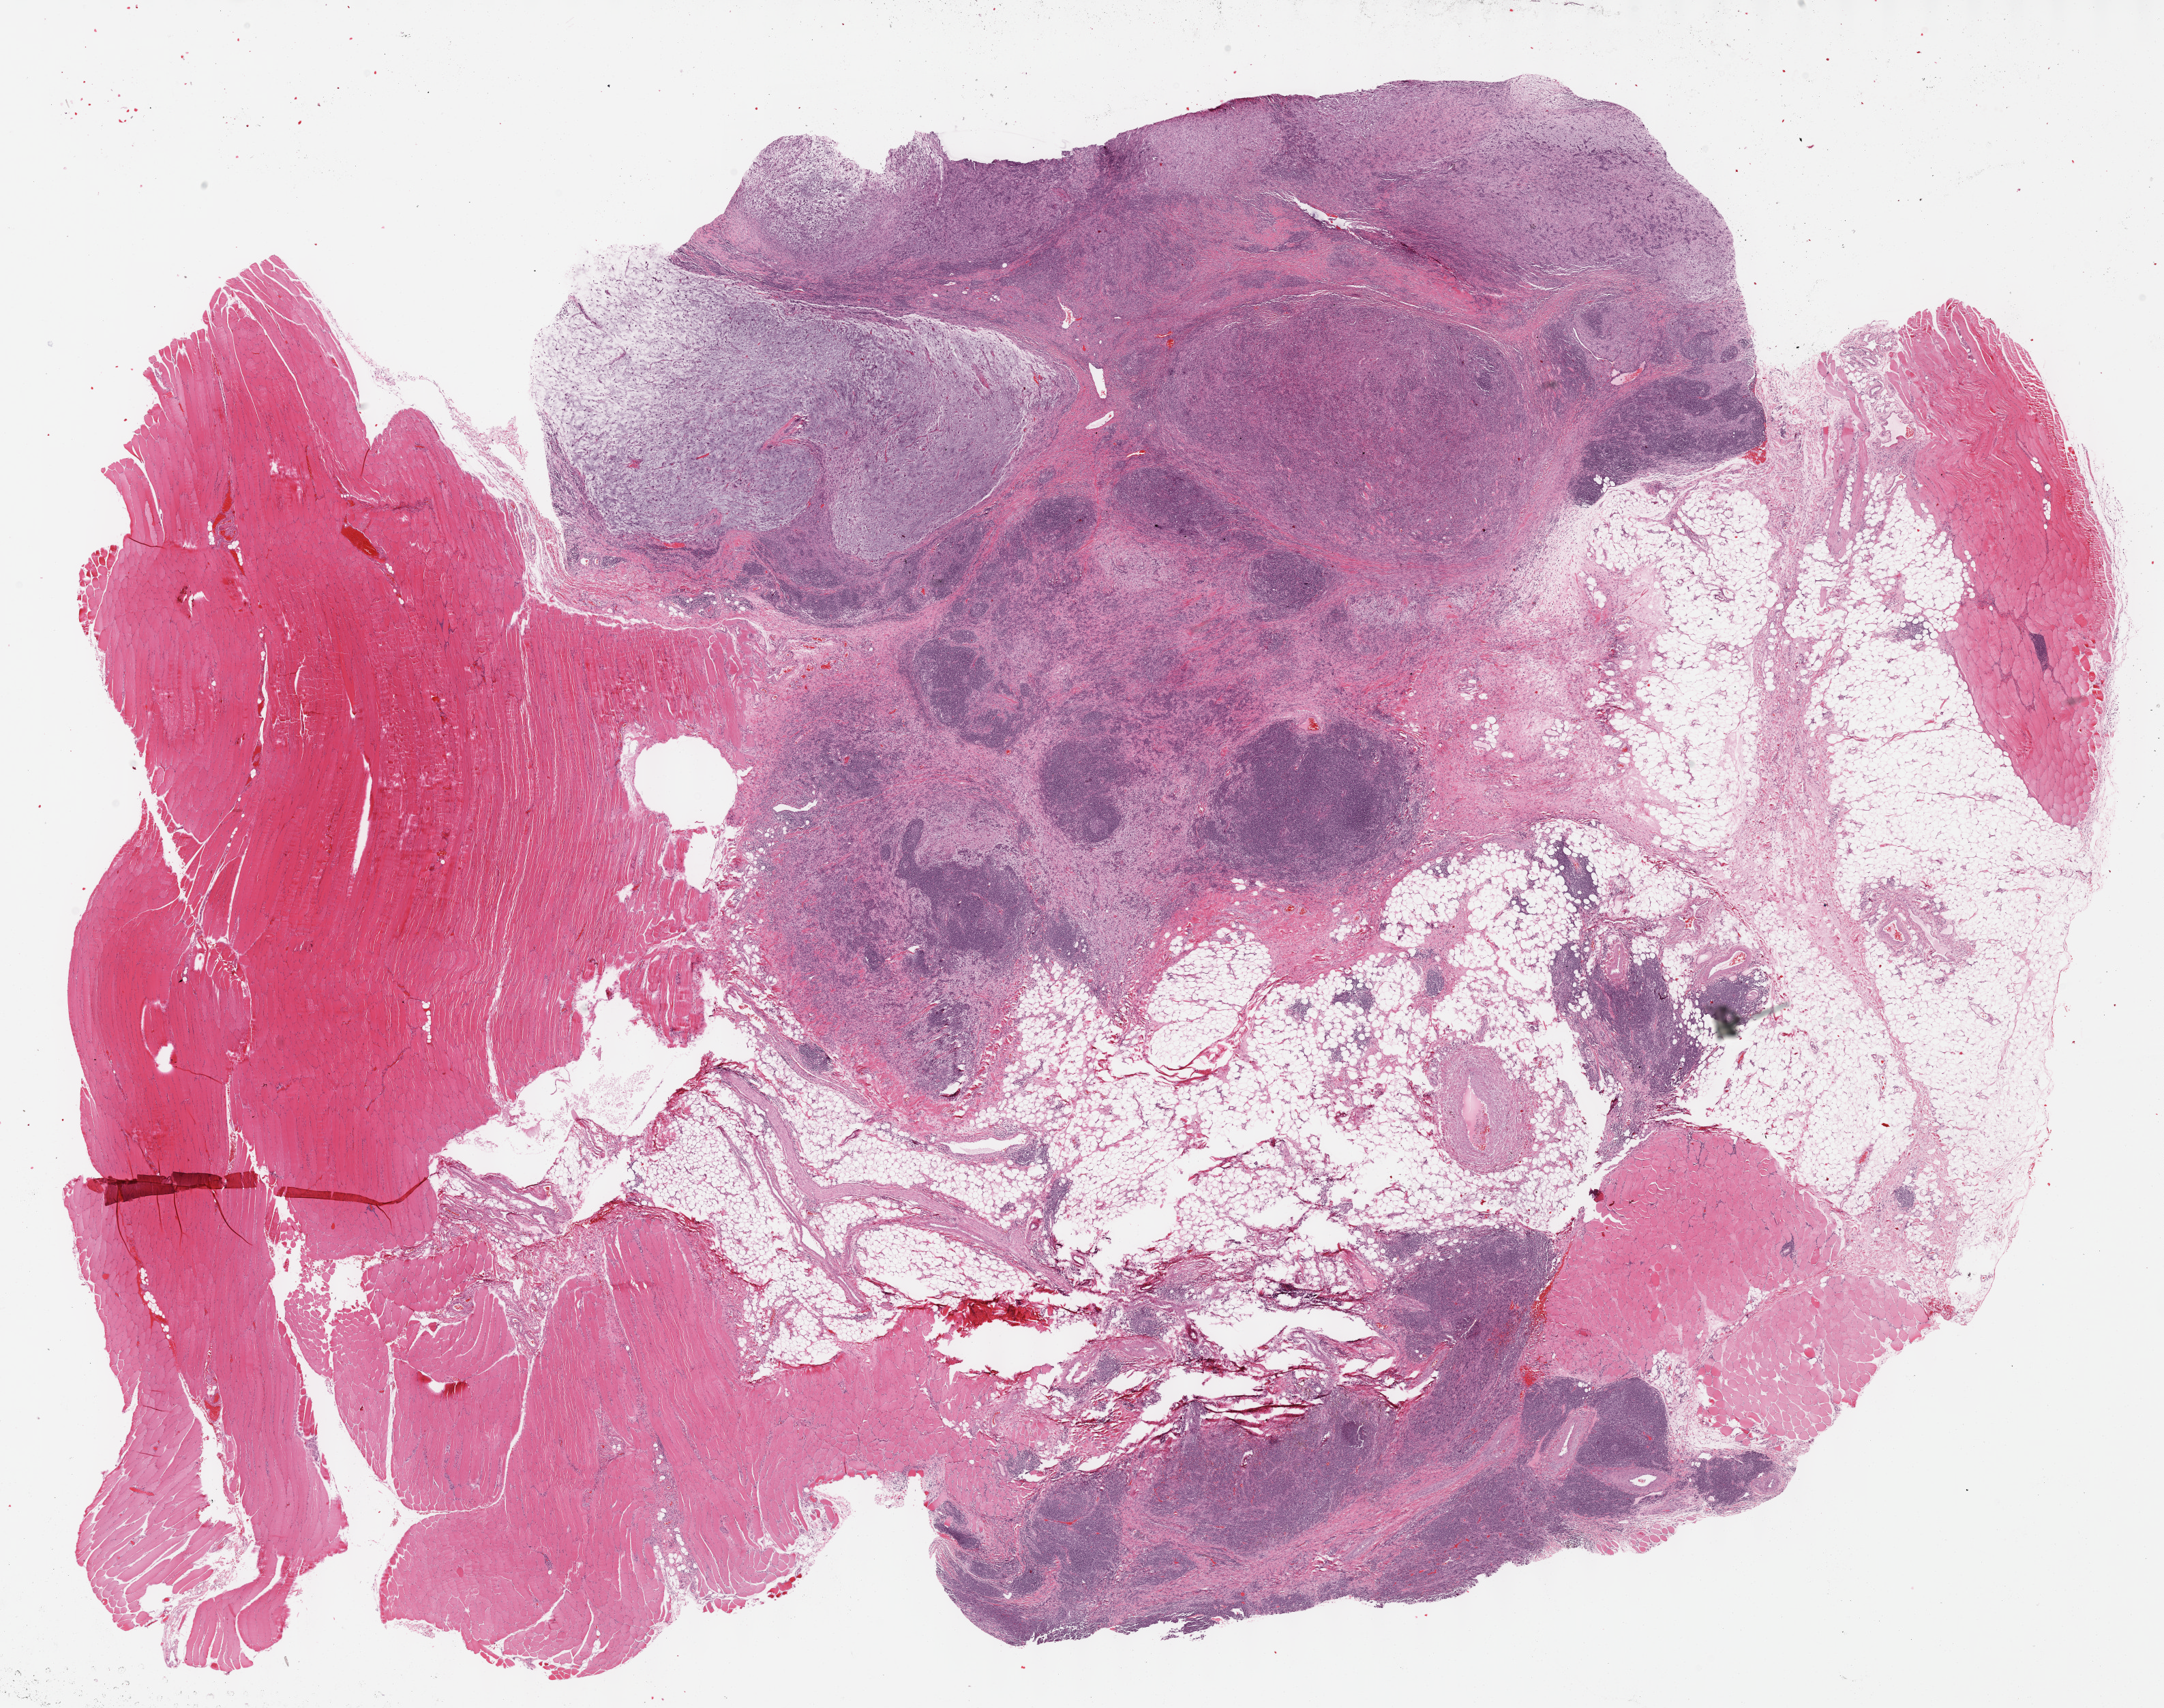
Whole-slide histology image, Hematoxylin and eosin (H&E) stained — low-resolution overview of the scanned area, about 25.7 x 20.2 mm. Formalin-fixed paraffin-embedded (FFPE) diagnostic section. Sample: primary tumour, connective, subcutaneous and other soft tissues. Patient: male, age at initial diagnosis 59 years.
Histologic diagnosis: Undifferentiated sarcoma (connective, subcutaneous and other soft tissues of upper limb and shoulder).